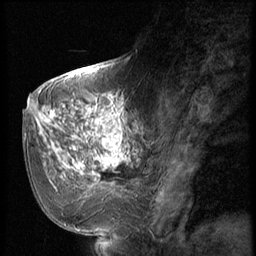
Breast MRI (dynamic contrast-enhanced), one sagittal slice; slice 23 of 56 in the series (ordered by position); dynamic contrast-enhanced series, image 2 of 2 at this slice position (ordered by acquisition); 1.5 T; TE 4.2 ms, TR 9 ms; 2.5 mm slice thickness; 256 × 256 image matrix. Patient: female, 51 years. From the clinical record (not read from this slice): setting: breast cancer imaged before/during neoadjuvant chemotherapy; receptor status: triple-negative.
Outlined on this slice (semi-automatically segmented with operator editing):
- analysis volume of interest (the breast-tissue region the enhancement analysis was run in; not a lesion): box from (x=60, y=98) to (x=147, y=197) px
- tumour enhancement mask (voxels above the 140 % enhancement threshold inside the analysis volume of interest): (x=64, y=102)–(x=129, y=175)